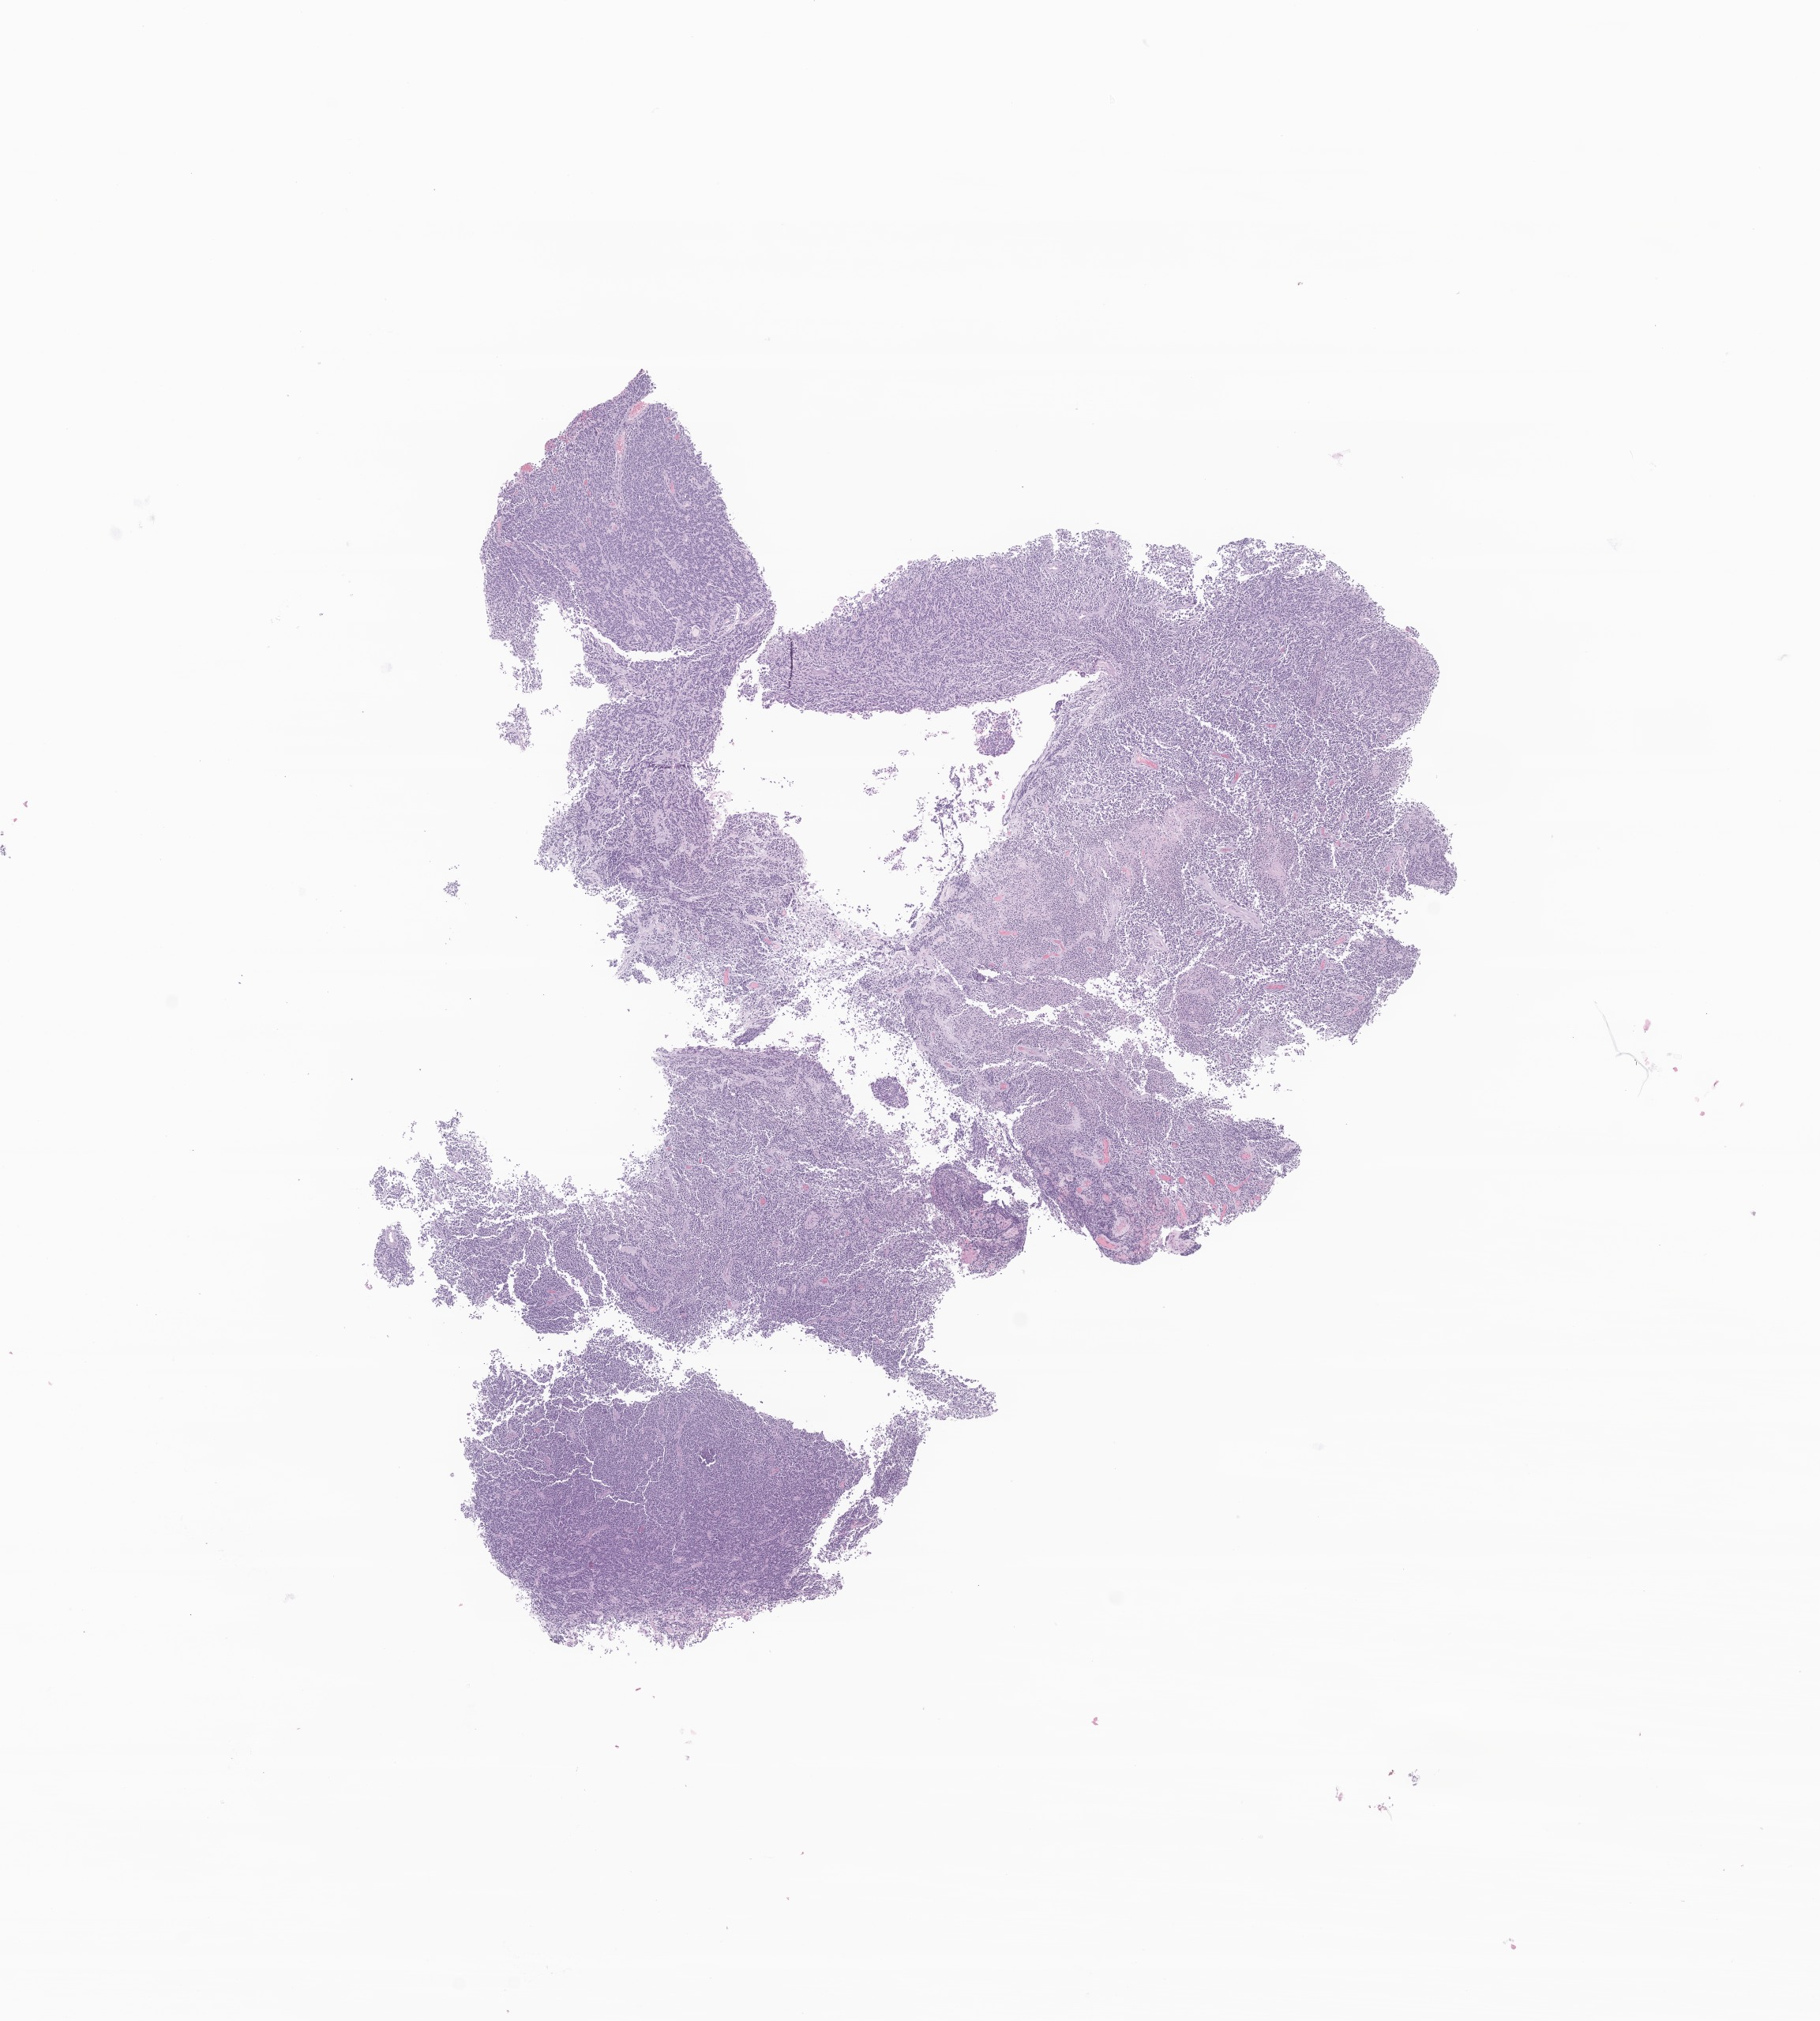
Whole-slide image, haematoxylin and eosin stain of tumor tissue from the brain — whole scanned area (about 9.7 x 10.8 mm) shown as a low-resolution overview; FFPE section. Patient: male, age 57 months.
Diagnosis (ICD-O-3 morphology term): Neoplasm, uncertain whether benign or malignant.